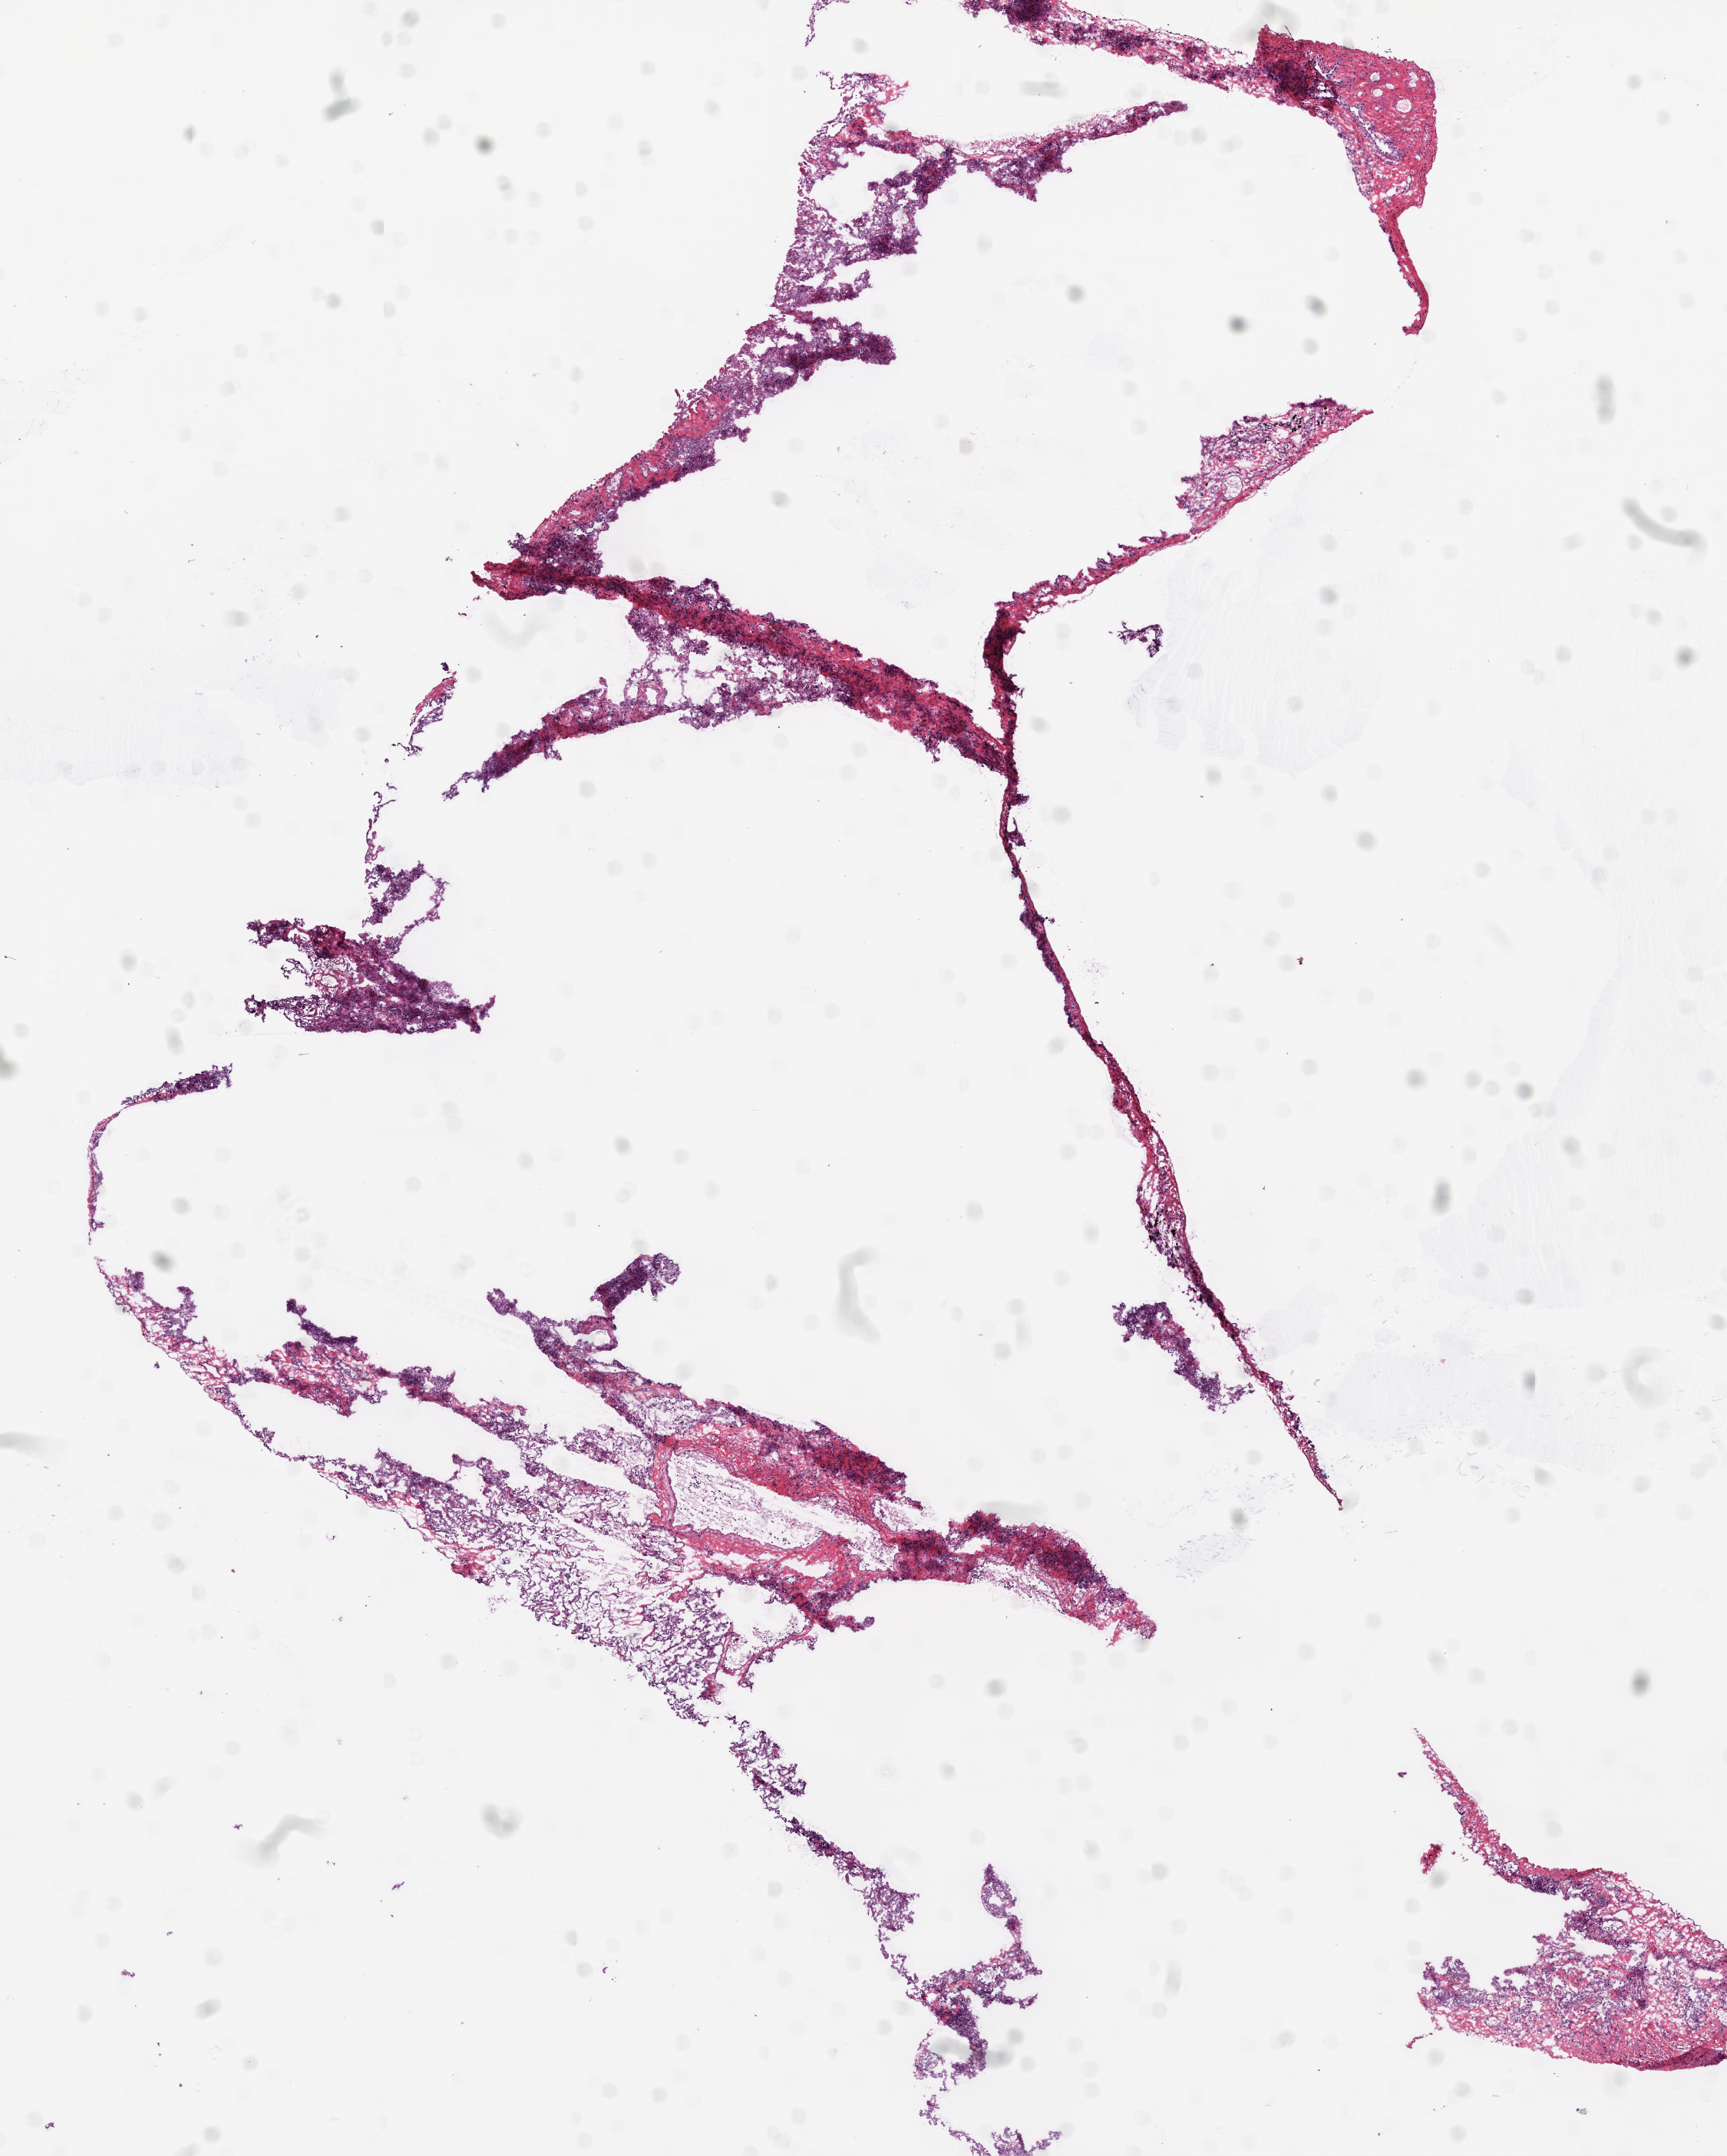
Whole-slide histology image, H&E — shown as a low-resolution overview of the whole scanned area (about 9.0 x 11.3 mm, acquisition: 20x scan); frozen section; sample: solid tissue normal (non-tumour tissue), lung. Patient: male, age at initial diagnosis 62 years.
This section: solid tissue normal (non-tumour) sample from the same patient. Patient diagnosis: Squamous cell carcinoma, NOS (lower lobe, lung).